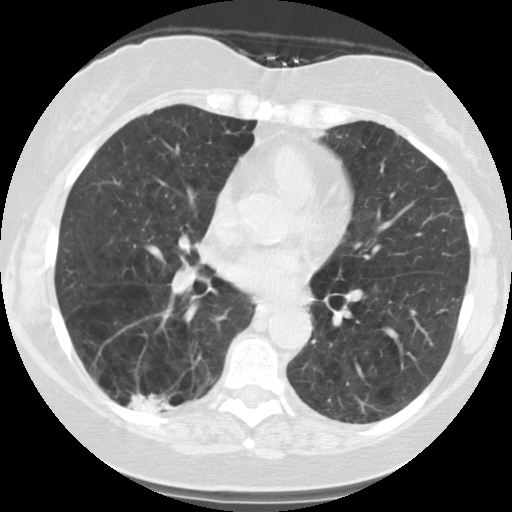
Low-dose screening chest CT, one axial slice. Slice 56 of 122 in the series (ordered by position). Reconstruction kernel STANDARD. 140 kVp. Lung window (W 1500 / L -600 HU). 2.5 mm slice thickness. 512 × 512 image matrix.
Structures marked on this image (outlined manually by an expert reader):
- lesion 1 (tumor, lower lobe of right lung): bounding box (x1, y1, x2, y2) in pixels: (126, 393, 174, 412)